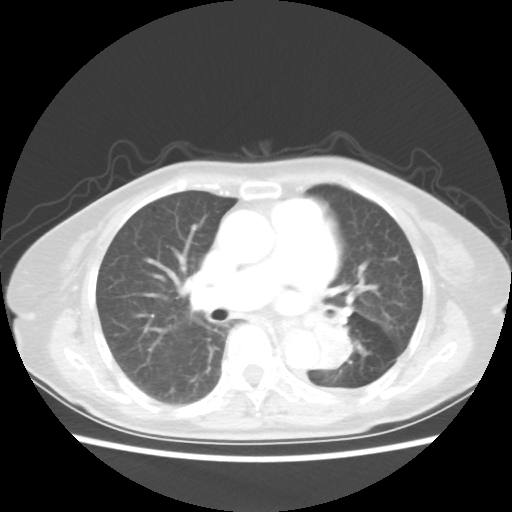
Chest CT, one axial slice. Position 27 of 50 along the scan axis. Reconstruction kernel STANDARD. 80 kVp. Lung window (W 1500 / L -600 HU). 5 mm slice thickness. 512 × 512 image matrix. Female patient, age 81 years. Case-level facts recorded for this patient, not image findings: clinical TNM (as recorded): T2 N0 M1a.
Outlined on this slice (bounding box drawn by a radiologist):
- lung tumour (recorded histology: squamous cell carcinoma): bounding box (x1, y1, x2, y2) in pixels: (307, 316, 359, 375)